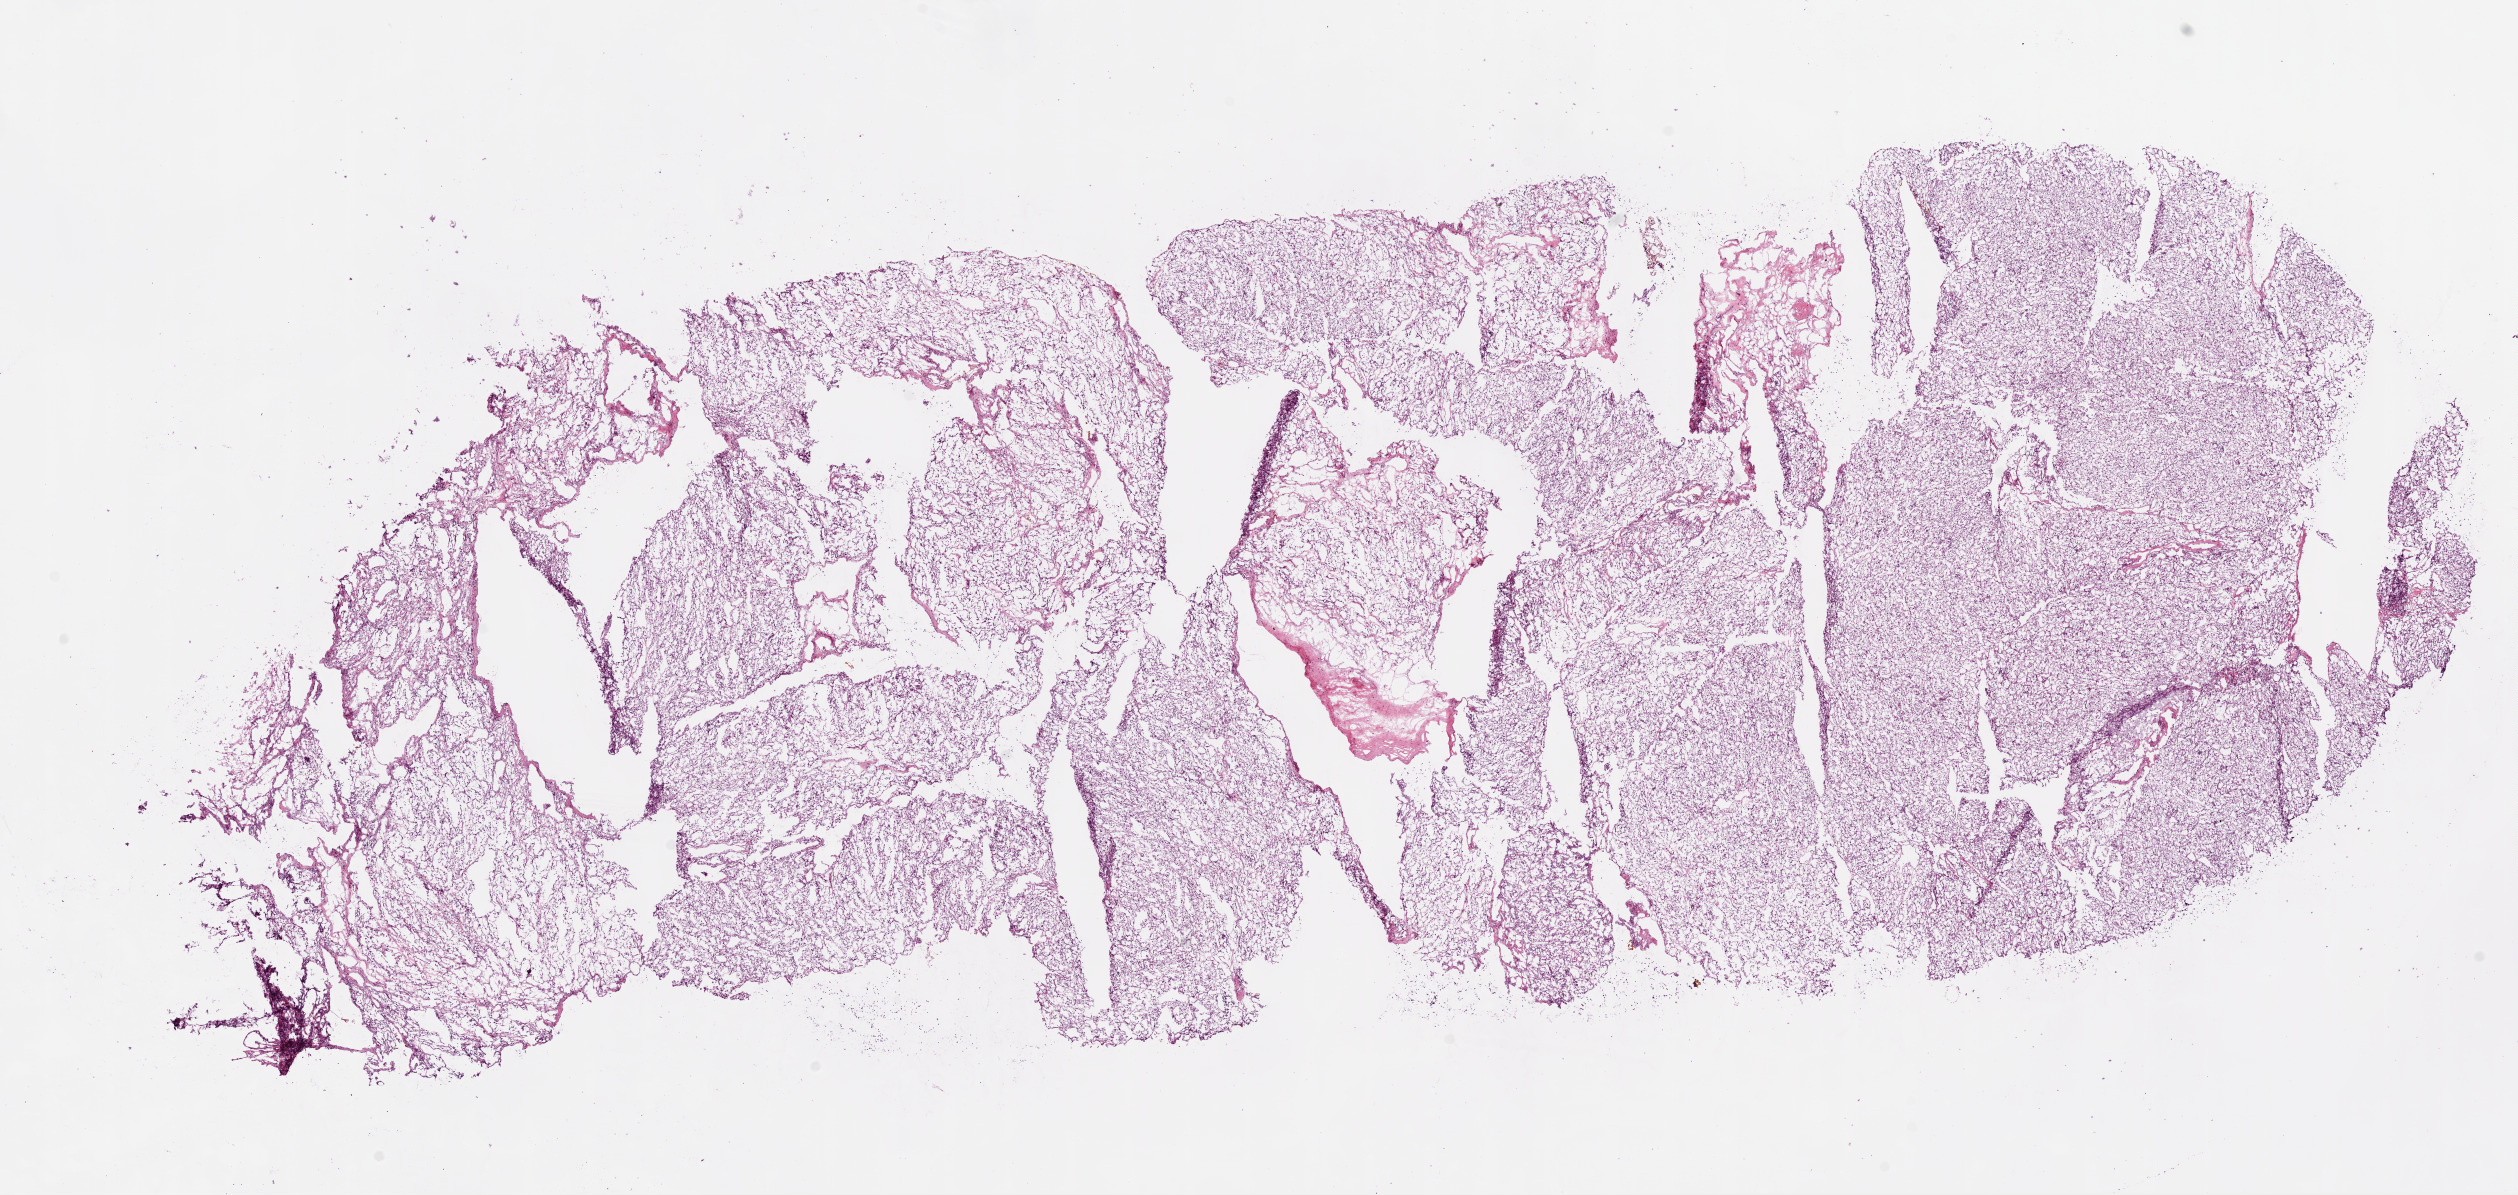
Whole-slide histology image, H&E, shown as a low-resolution overview of the whole scanned area (about 20.3 x 9.6 mm); frozen section from the top of the tissue portion; primary tumour sample from the kidney. Male, age 61 years at initial diagnosis. Histologic grade: G2 (moderately differentiated). Slide review estimates, as recorded: tumour cells 92%, tumour nuclei 85%, normal cells 0%, stromal cells 8%, necrosis 0%.
- AJCC pathologic stage: III
- diagnosis: Clear cell adenocarcinoma, NOS